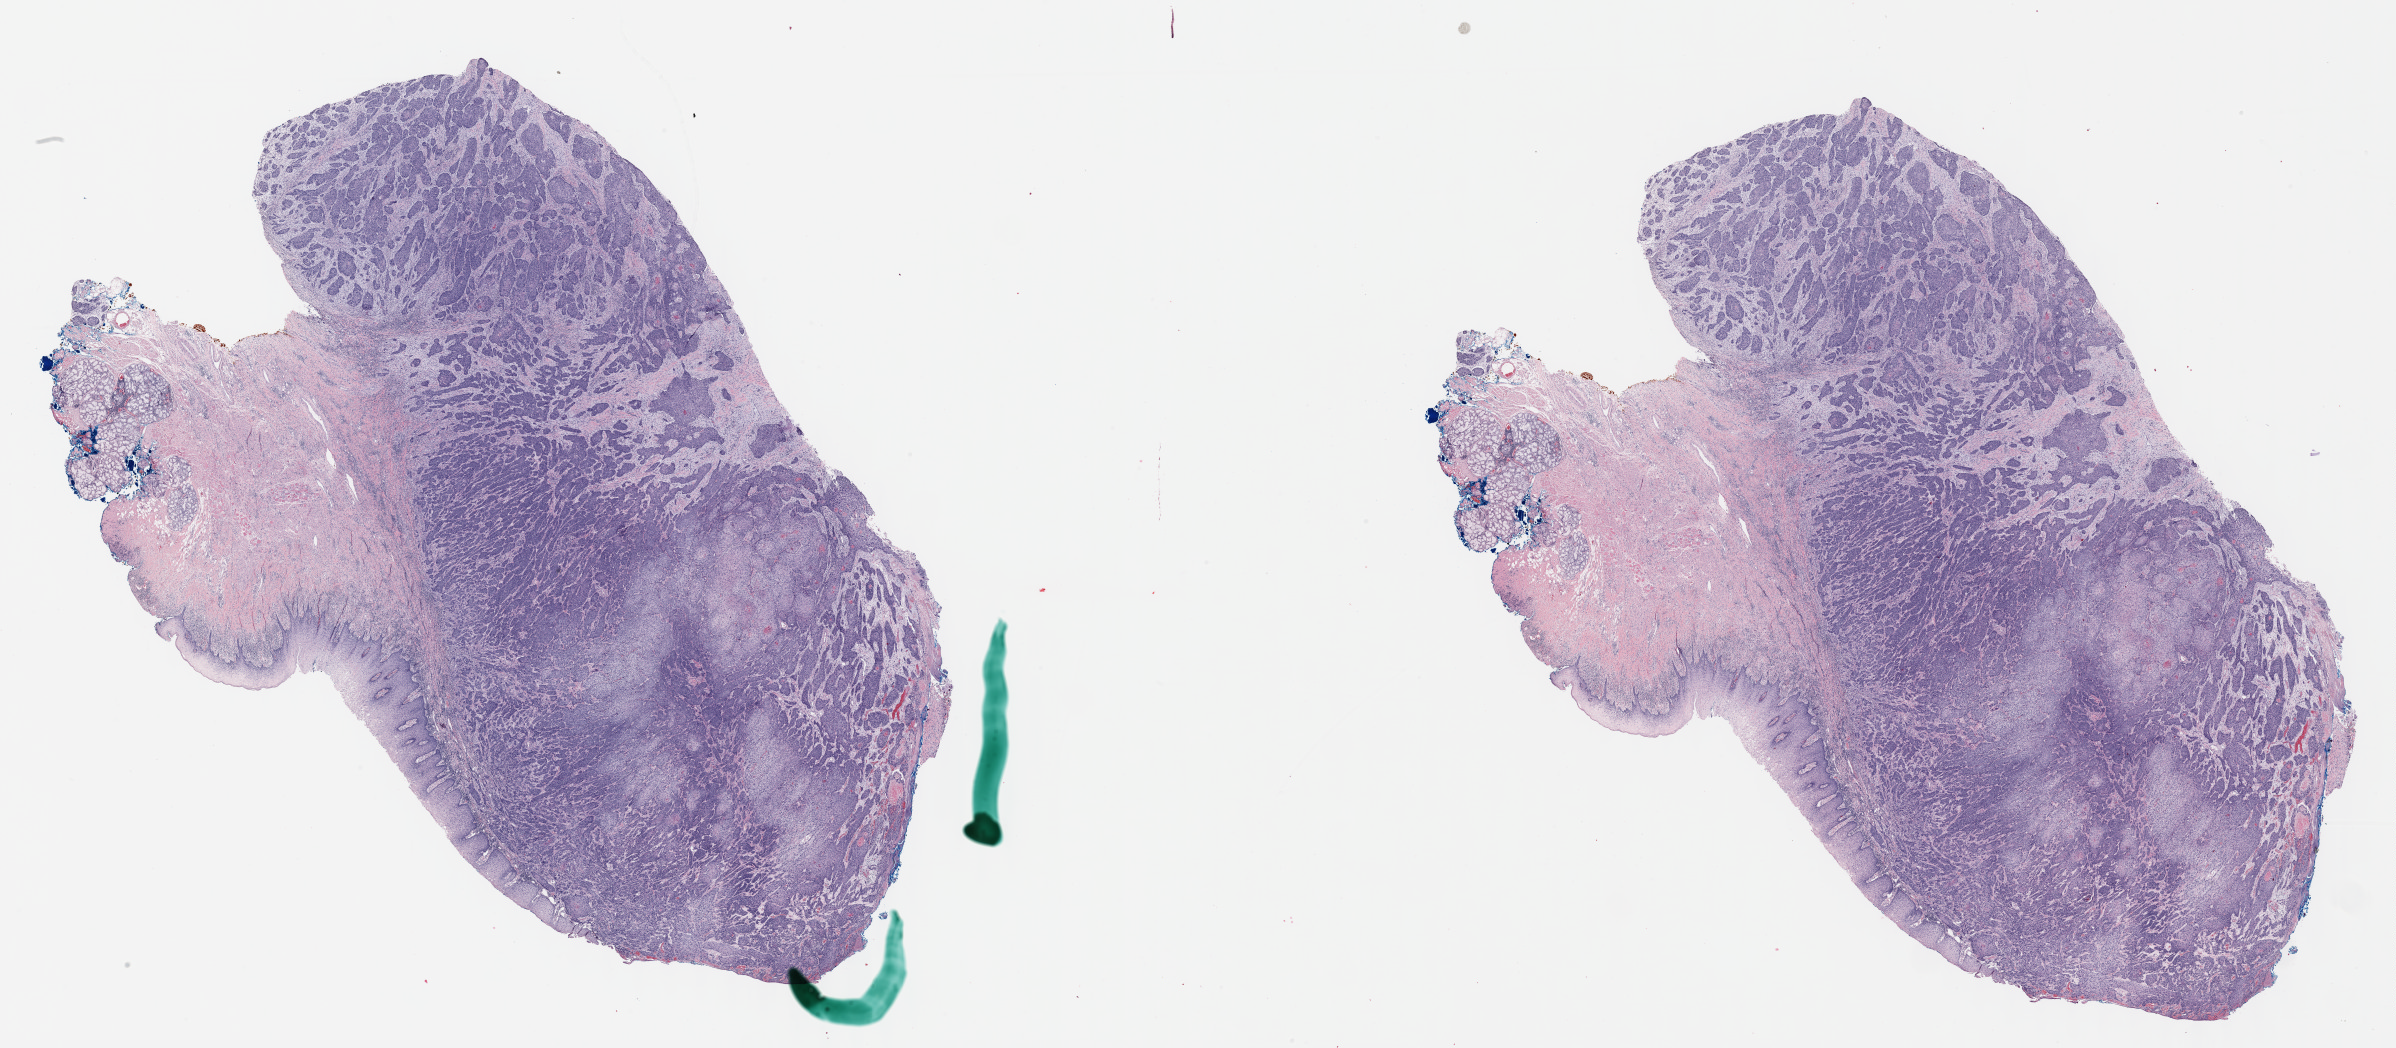
Whole-slide histology image, Hematoxylin and eosin (H&E) stained — low-resolution overview of the scanned area, about 38.7 x 16.9 mm (acquisition: 40x scan). Formalin-fixed paraffin-embedded (FFPE) diagnostic section. Head and neck, primary tumour sample. Female, age 53 years at initial diagnosis.
Histologic diagnosis: Squamous cell carcinoma, keratinizing, NOS.